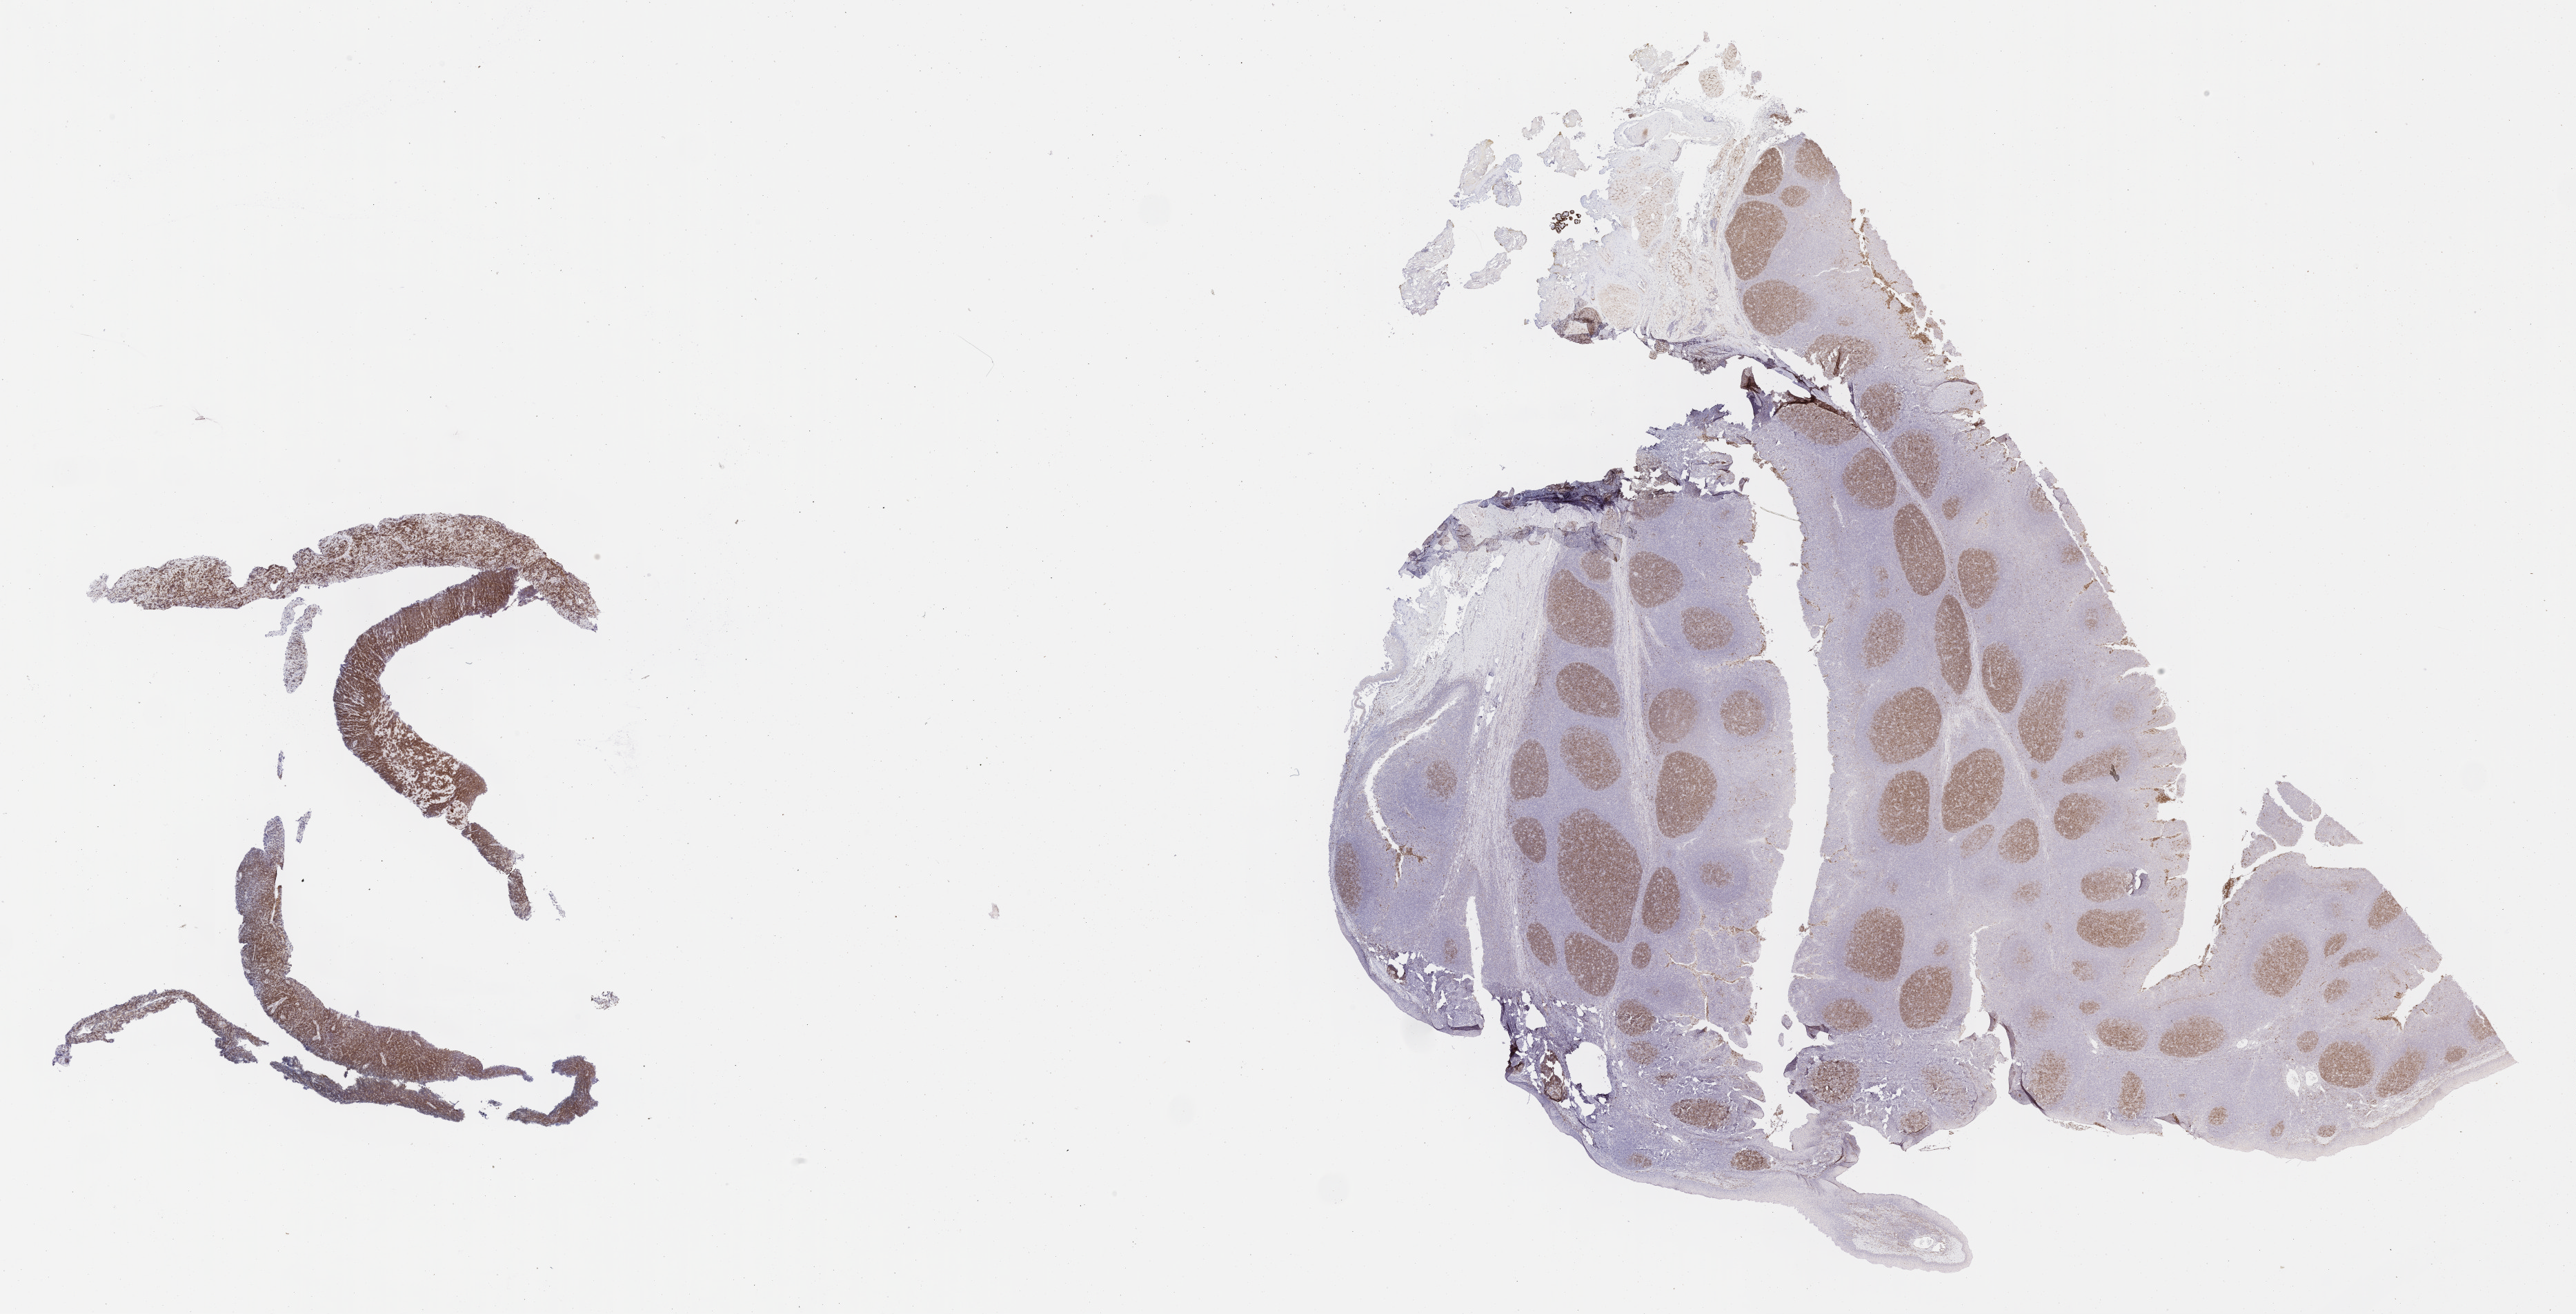
Immunohistochemistry (IHC) whole-slide image stained for CD10, shown as a low-resolution overview of the whole scanned area (about 30.2 x 15.4 mm), tumor tissue, site: pleura. Male, age 2 years at initial diagnosis.
Histologic diagnosis: Diffuse large B-cell lymphoma, NOS.